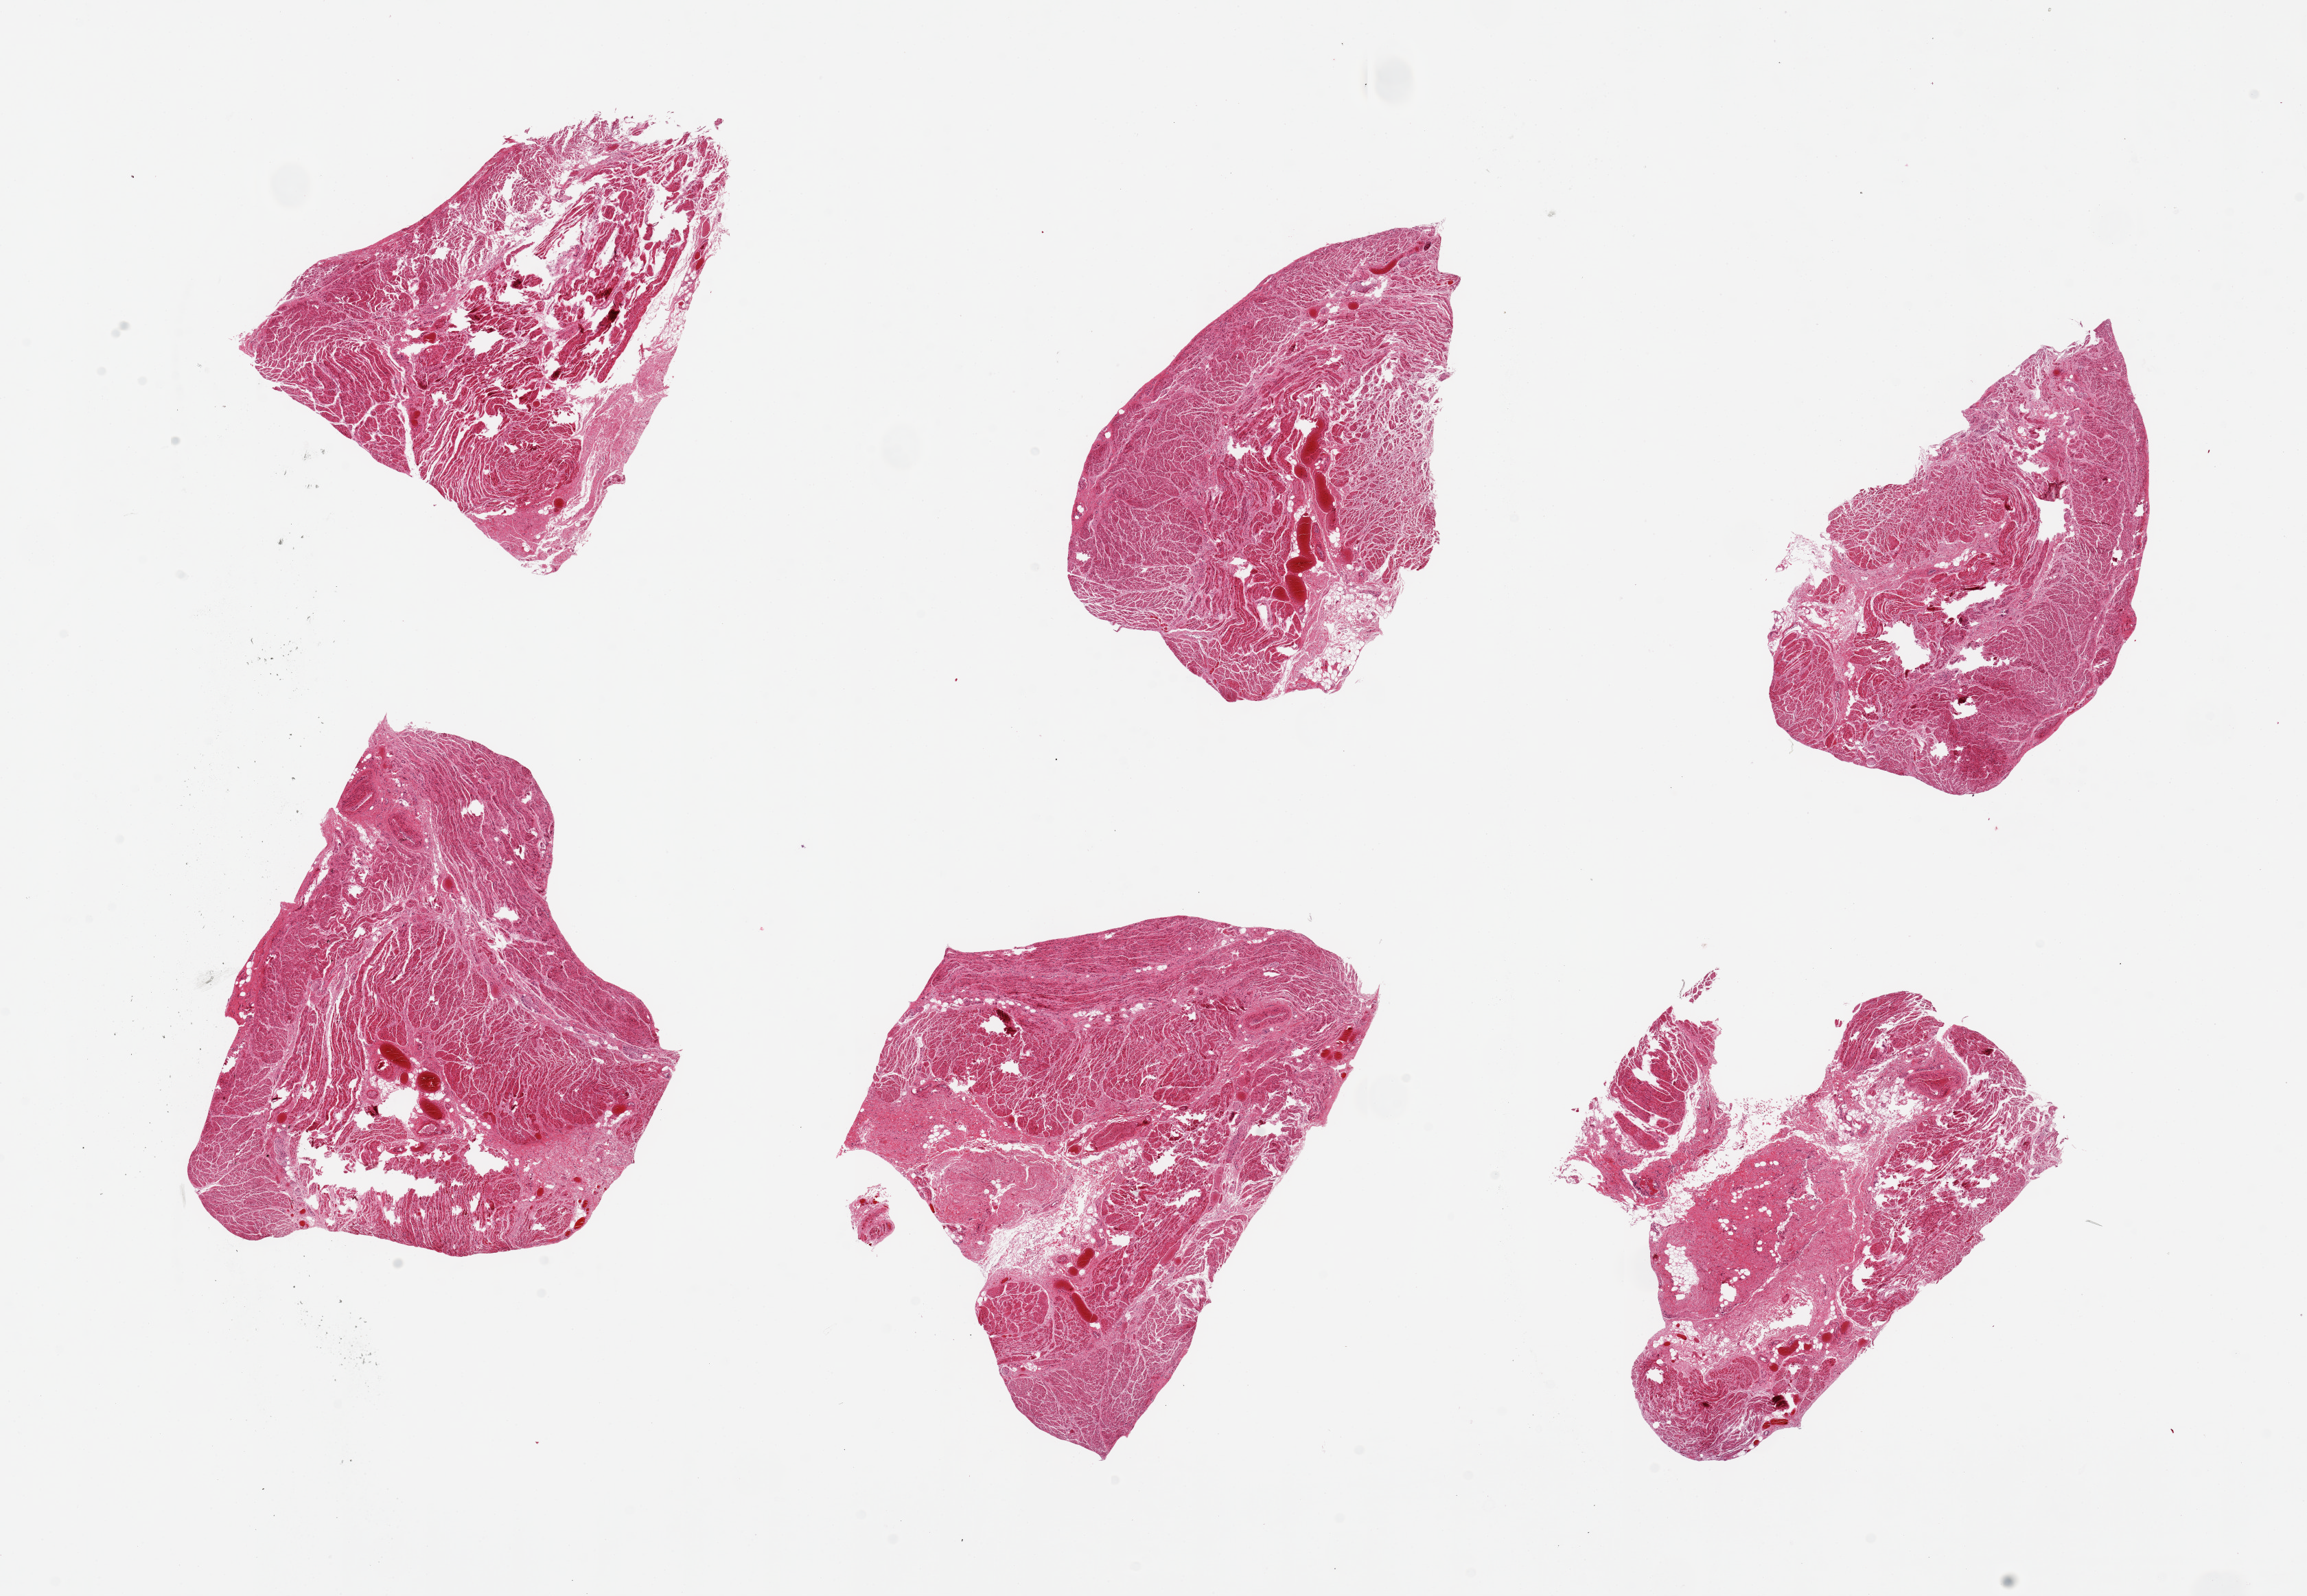
Whole-slide image, H&E stain, brightfield, low-resolution overview of the scanned area, about 26.6 x 18.4 mm (acquisition: 20x scan). PAXgene-fixed, paraffin-embedded tissue. Sampled site (target tissue): gastroesophageal junction. Donor tissue sample.
Review note (as recorded): 6 pieces; up to 6.5x5mm; muscle and submucosa with fibrovascular stroma in 2 pieces up to 2mm in diameter.